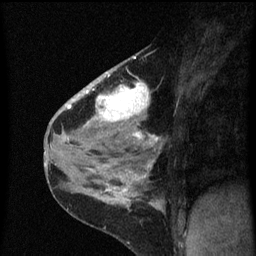
Breast MRI (dynamic contrast-enhanced), one sagittal slice. Slice 37 of 60 in the series (ordered by position). Dynamic contrast-enhanced series, image 2 of 3 at this slice position (ordered by acquisition). 1.5 T. TE 4.2 ms, TR 8 ms. 256 × 256 image matrix, field of view 180 × 180 mm. Patient: female, 38 years.
Structures marked on this image (semi-automatic segmentation, software-assisted and operator-edited):
- analysis volume of interest (the breast-tissue region the enhancement analysis was run in; not a lesion): box from (x=80, y=52) to (x=163, y=151) px
- tumour enhancement mask (voxels above the 70 % enhancement threshold inside the analysis volume of interest): (x=80, y=56)–(x=159, y=147)